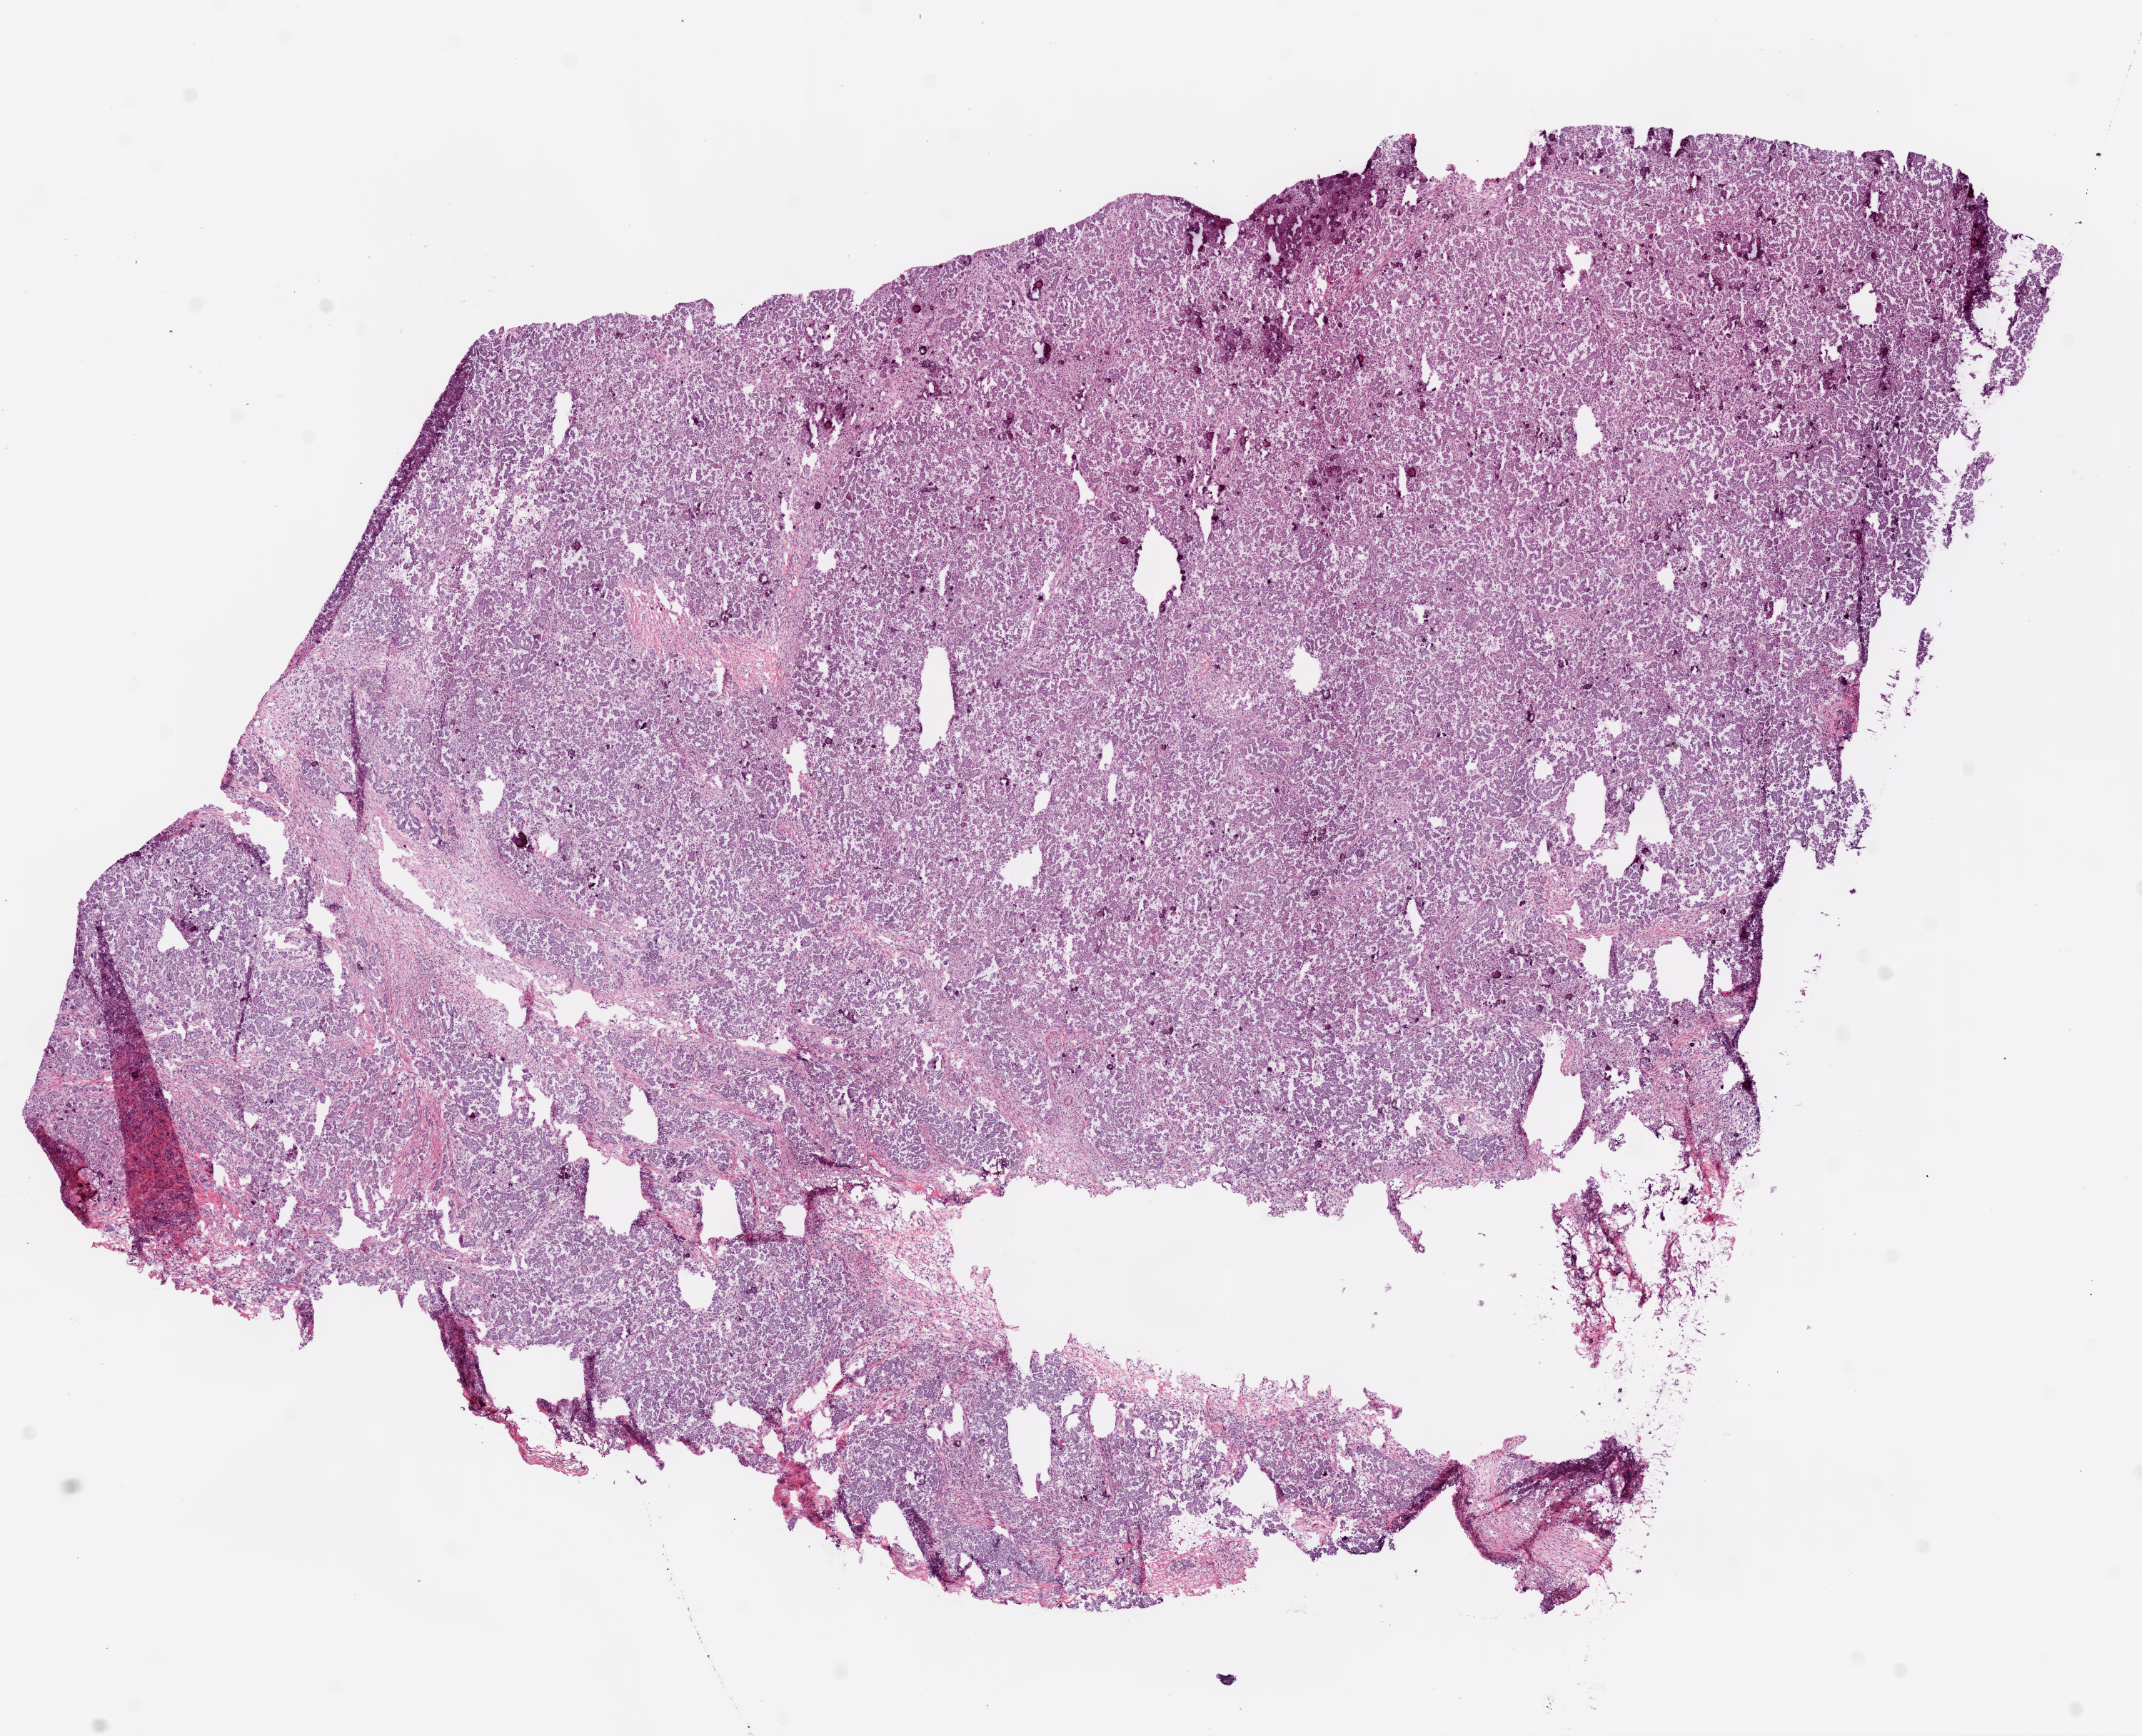
Whole-slide histology image, H&E-stained, low-resolution overview of the scanned area, about 12.0 x 9.8 mm (slide scanned at 20x); frozen section; ovary, primary tumour sample. Female patient; age at initial diagnosis 26 years. Histologic grade: G1 (well differentiated). Composition of this section per pathologist review: tumour cells 92%, tumour nuclei 85%, normal cells 0%, stromal cells 8%, necrosis 0%.
• pathologic diagnosis: Serous cystadenocarcinoma, NOS
• FIGO stage: IIIC